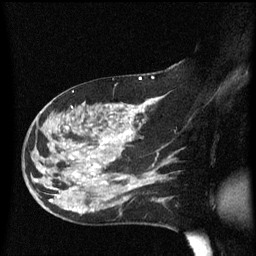
Breast MRI (dynamic contrast-enhanced), one sagittal slice. Dynamic contrast-enhanced series, image 2 of 3 at this slice position (ordered by acquisition). 1.5 T. TE 4.2 ms, TR 8.4 ms. 2.2 mm slice thickness. 256 × 256 image matrix, field of view 200 × 200 mm. Female patient, age 47 years.
Outlined on this slice (semi-automatically segmented with operator editing):
- analysis volume of interest (the breast-tissue region the enhancement analysis was run in; not a lesion): bounding box <22,97,149,206> (left, top, right, bottom; pixels)
- tumour enhancement mask (voxels above the 70 % enhancement threshold inside the analysis volume of interest): <36,101,149,203>